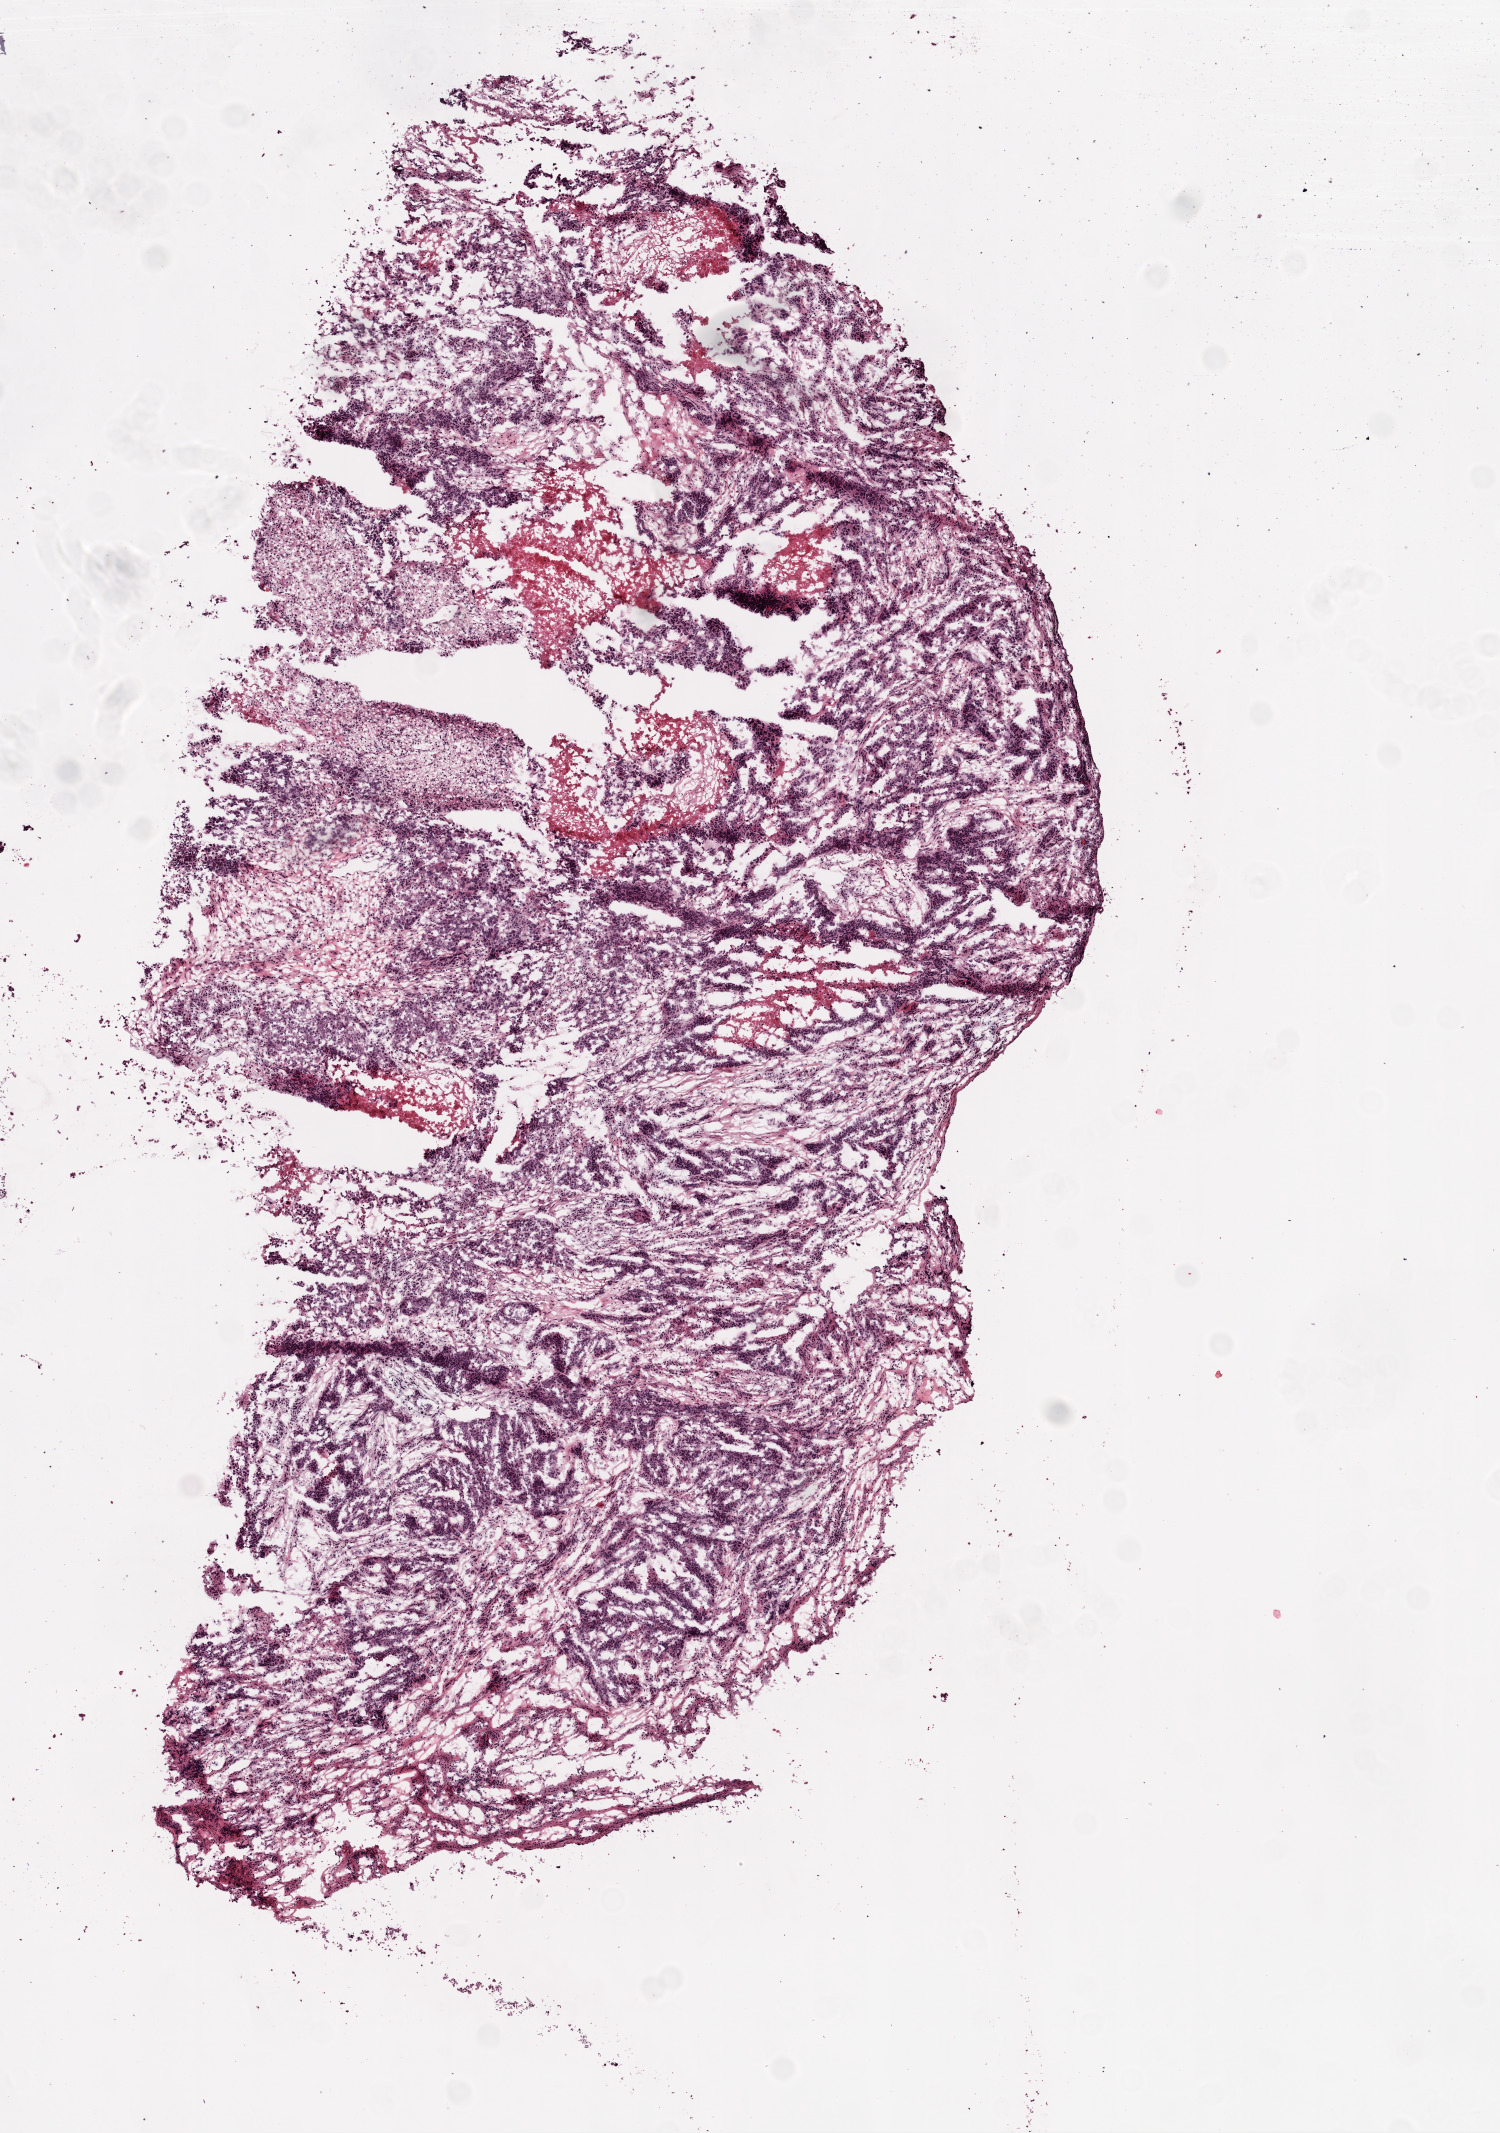
H&E whole-slide image, low-resolution overview of the scanned area, about 6.0 x 8.6 mm (from a 20x scan), frozen section from the top of the tissue portion, primary tumour sample from the ovary. Patient: female, age at initial diagnosis 79 years. Histologic grade: G3 (poorly differentiated). Pathologist review of this section (percent, as recorded): tumour cells 80%, tumour nuclei 90%, normal cells 0%, stromal cells 10%, necrosis 10%.
- laterality: right
- pathologic diagnosis: Serous cystadenocarcinoma, NOS
- FIGO stage: IIIC